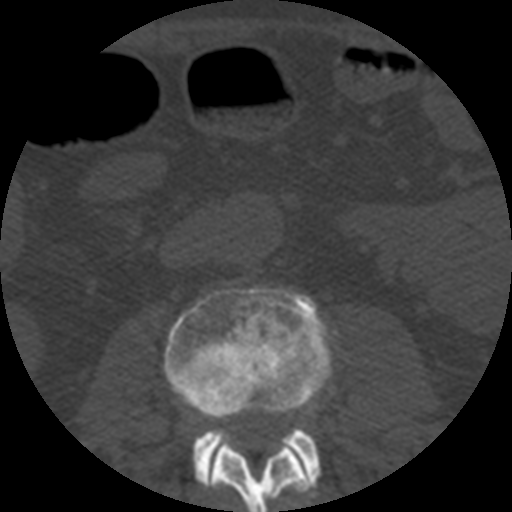
CT including the spine, one axial slice; bone window (W 1800 / L 400 HU); 512 × 512 image matrix. Patient age 57 years. Case-level facts recorded for this patient, not image findings: primary cancer: prostate.
Outlined on this slice (semi-automatically segmented with operator editing):
- L2 vertebra: bounding box [x1, y1, x2, y2] px = [201, 429, 316, 512]
- L3 vertebra: [165, 287, 331, 483]